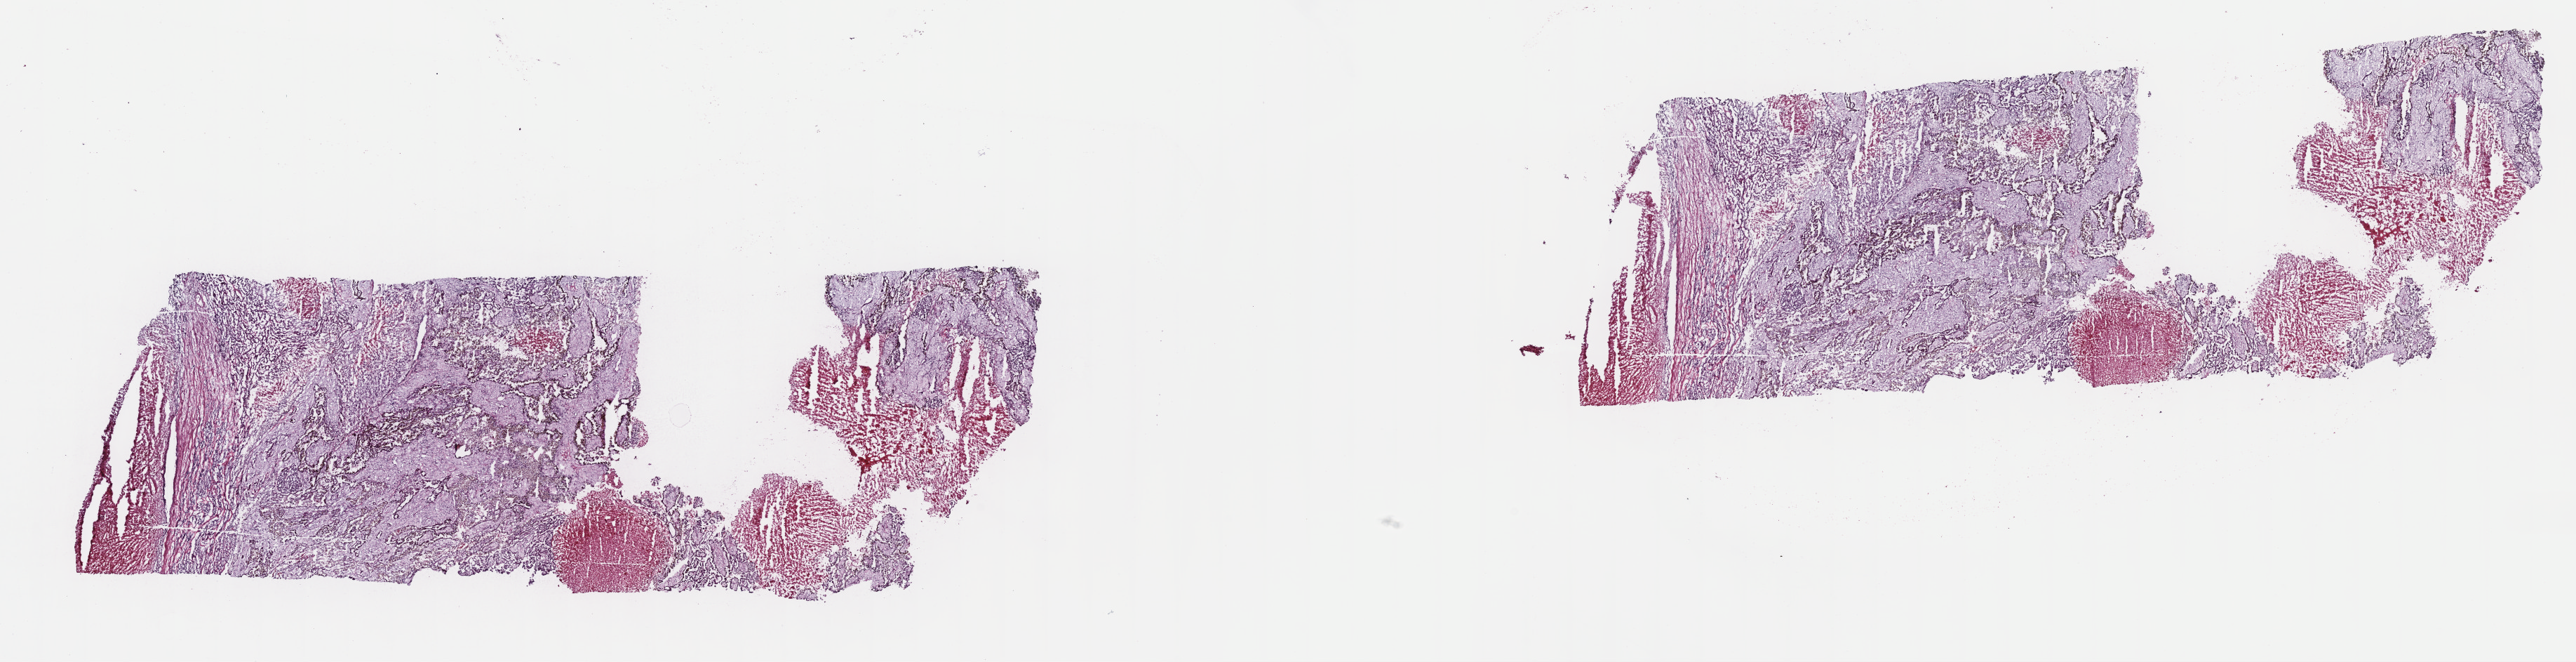
H&E-stained whole-slide image — low-resolution overview of the scanned area, about 29.7 x 7.6 mm (acquisition: 40x scan). Frozen section from the top of the tissue portion. Primary tumour sample from the kidney. Male patient; age at initial diagnosis 62 years. Composition of this section per pathologist review: tumour cells 85%, tumour nuclei 75%, normal cells 0%, stromal cells 0%, necrosis 15%. Inflammatory infiltration, as recorded: lymphocyte infiltration 1%, monocyte infiltration 0%, neutrophil infiltration 0%.
• TNM: T2 N0 MX
• diagnosis: Papillary adenocarcinoma, NOS
• AJCC pathologic stage: II (6th edition)
• laterality: left